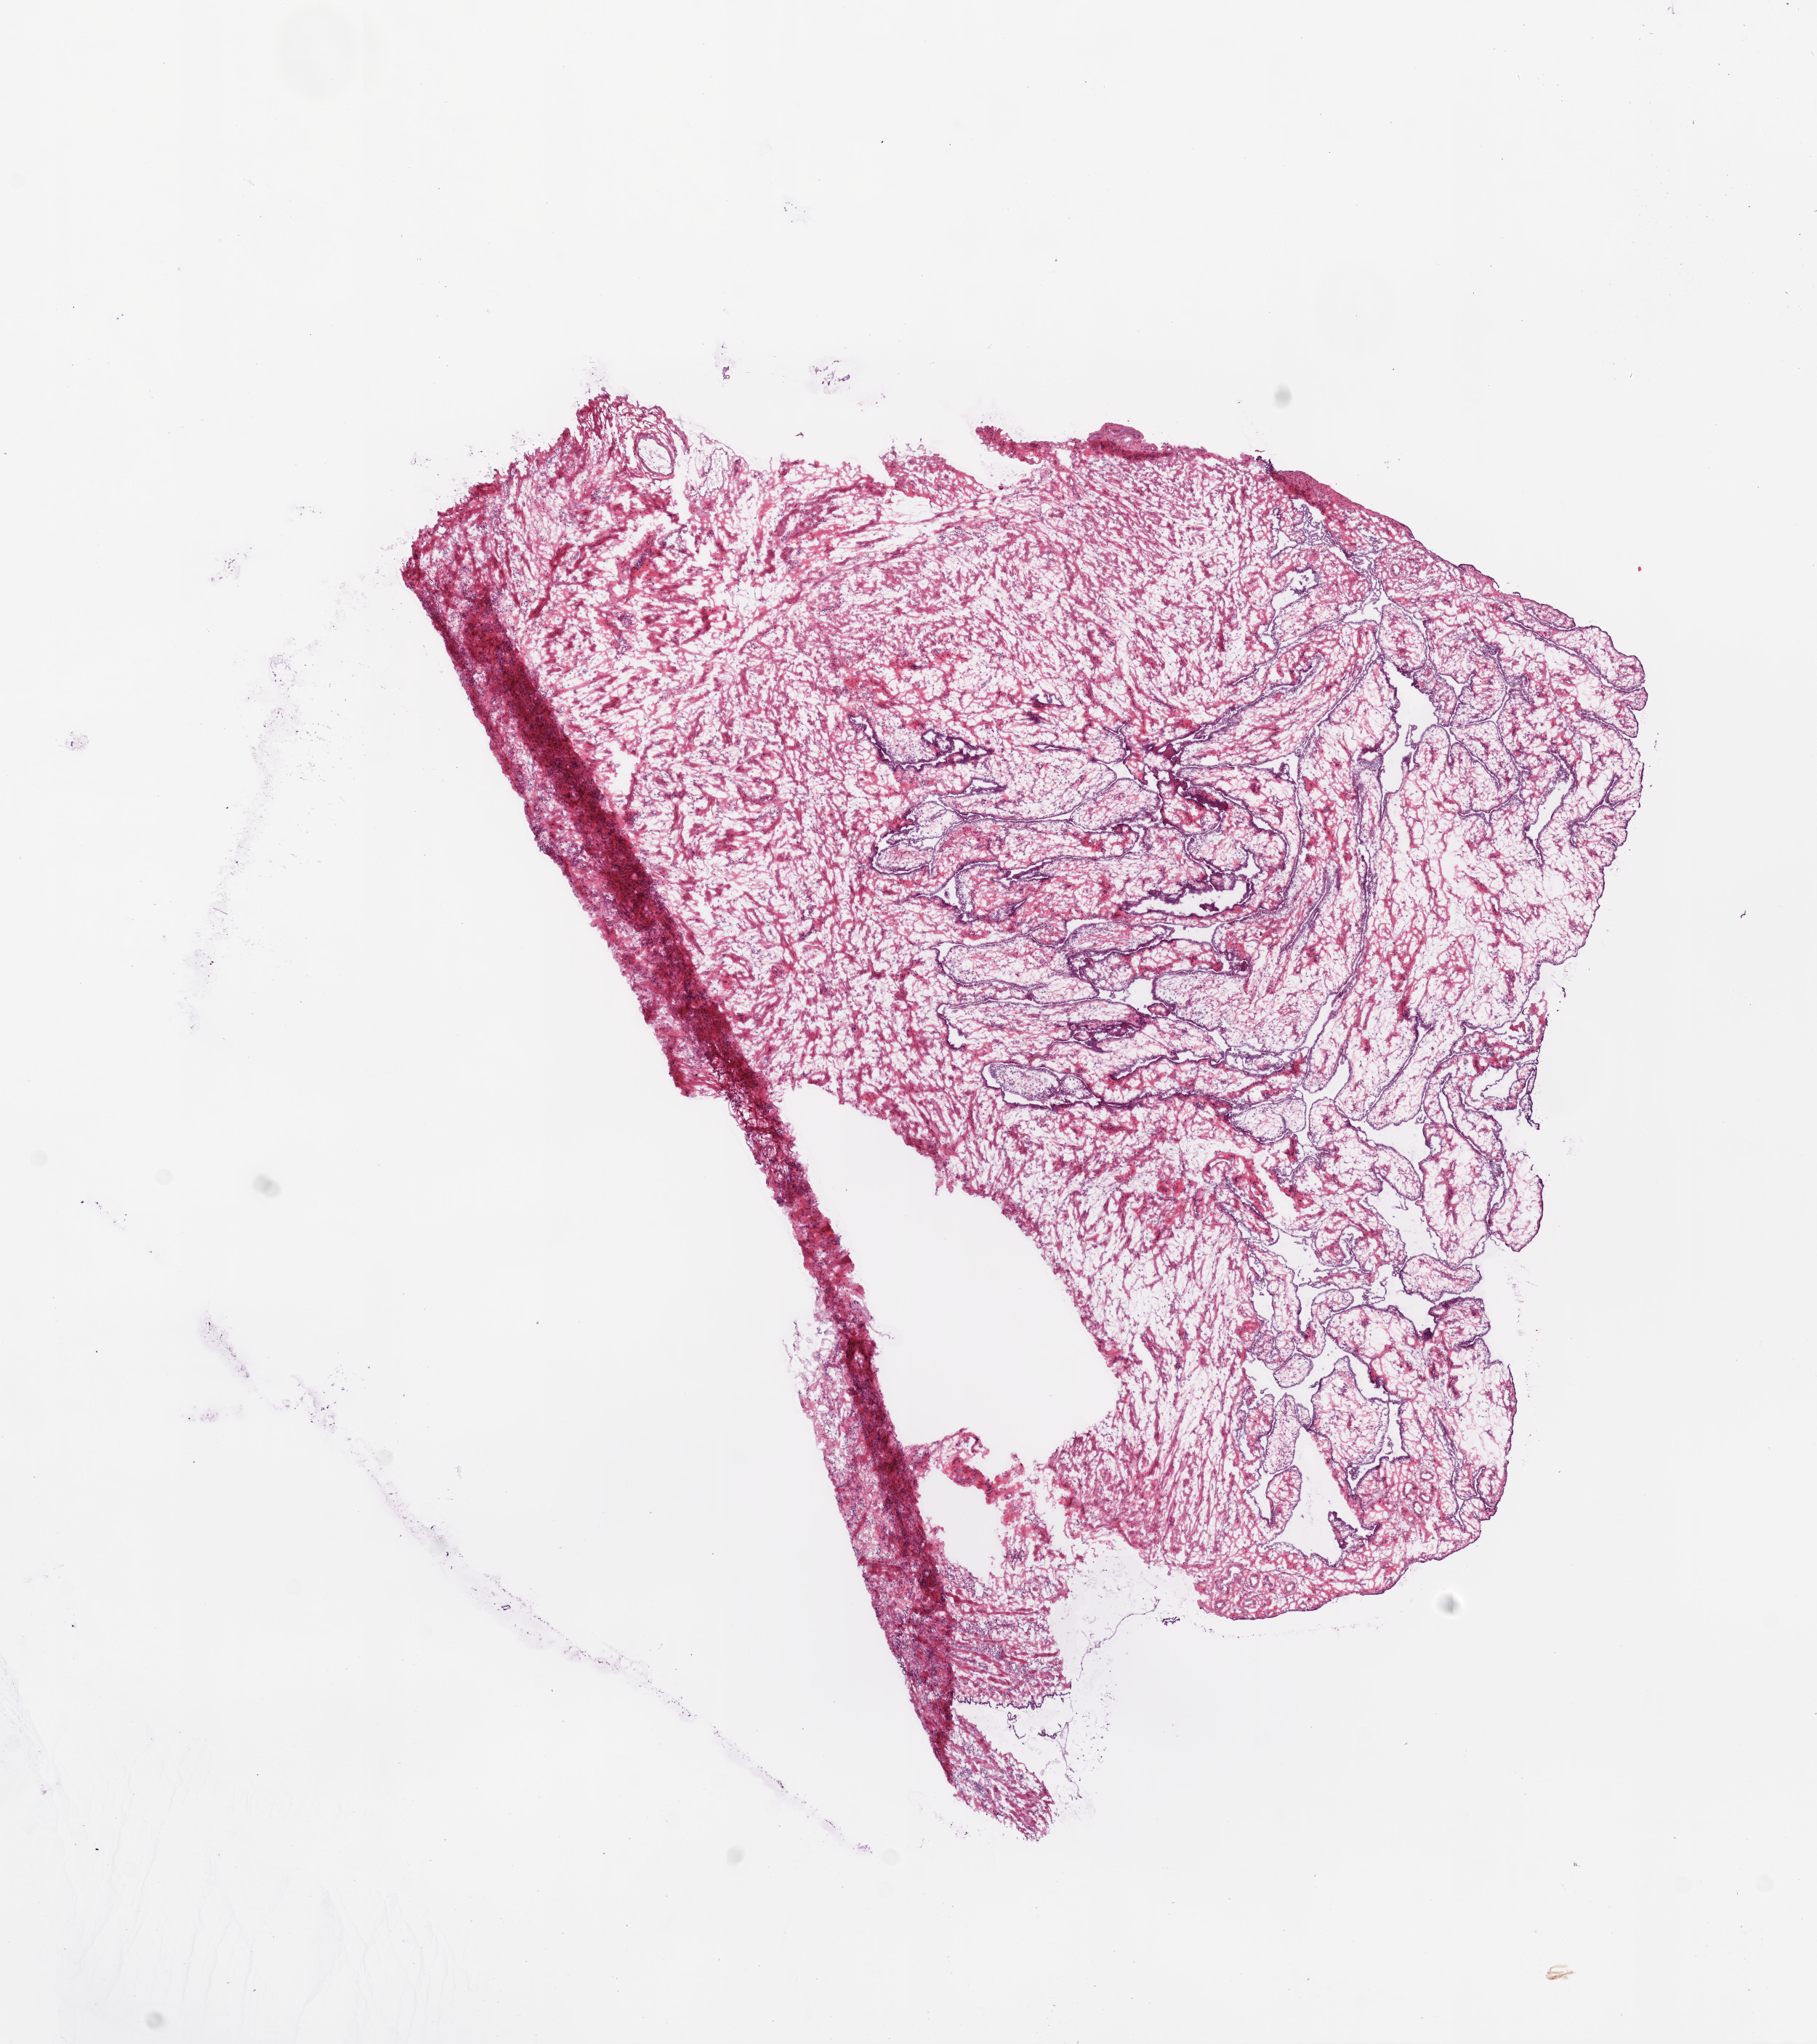
Whole-slide histology image, H&E-stained, shown as a low-resolution overview of the whole scanned area (about 10.0 x 11.3 mm); frozen section; ovary, solid tissue normal (non-tumour tissue) sample. Female patient; age at initial diagnosis 55 years.
* this section: solid tissue normal (non-tumour) sample from the same patient
* patient diagnosis: Serous cystadenocarcinoma, NOS